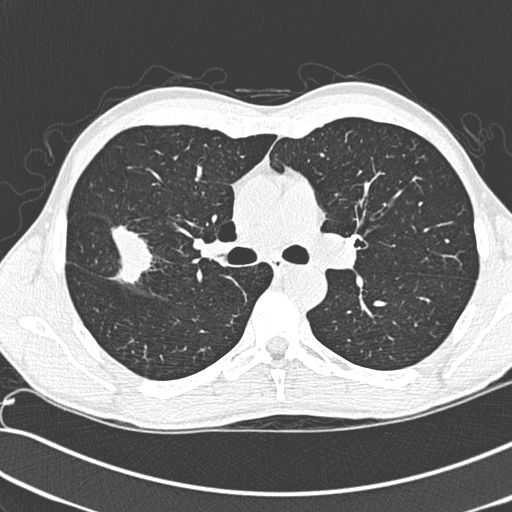
Low-dose screening chest CT, one axial slice; slice 188 of 281 in the series (ordered by position); 120 kVp; lung window (W 1500 / L -600 HU); 1.3 mm slice thickness; 512 × 512 image matrix, field of view 341 × 341 mm.
Outlined on this slice (outlined manually by an expert reader):
- lesion 1 (tumor, upper lobe of right lung): bounding box (x1, y1, x2, y2) in pixels: (111, 225, 153, 285)